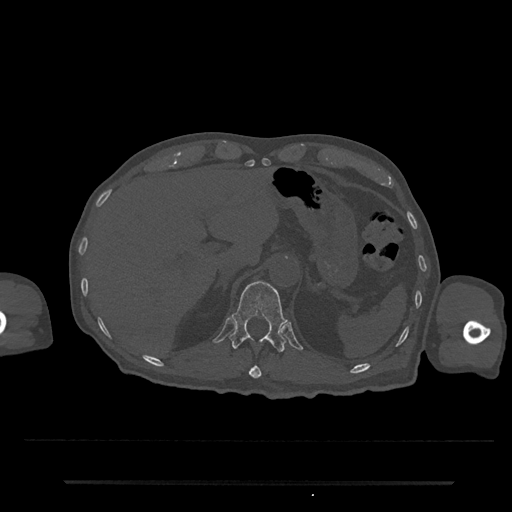
CT including the spine, one axial slice. Slice 208 of 797 in the series (ordered by position). Reconstruction kernel Br40s/3. Bone window (W 1800 / L 400 HU). 0.5 mm slice thickness. 512 × 512 image matrix. Patient: male, 74 years. From the clinical record (not read from this slice): primary cancer: prostate.
Structures marked on this image (semi-automatically segmented with operator editing):
- T11 vertebra: box from (x=249, y=365) to (x=262, y=379) px
- T12 vertebra: (x=230, y=281)–(x=287, y=352)